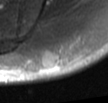
MRI of an extremity soft-tissue mass, one axial slice. Slice 11 of 42 in the series (ordered by position). T2-weighted fat-saturated. MR volume resampled by the dataset authors to the PET/CT grid (not the native acquisition matrix). 108 × 103 image matrix. Male patient. From the clinical record (not read from this slice): histological type: leiomyosarcoma; grade: intermediate; site of the primary tumour: left pelvis.
Outlined on this slice (expert contour drawn on MRI and transferred to this co-registered scan by the dataset authors):
- gross tumour volume (mass): bounding box [x1, y1, x2, y2] px = [44, 53, 61, 66]